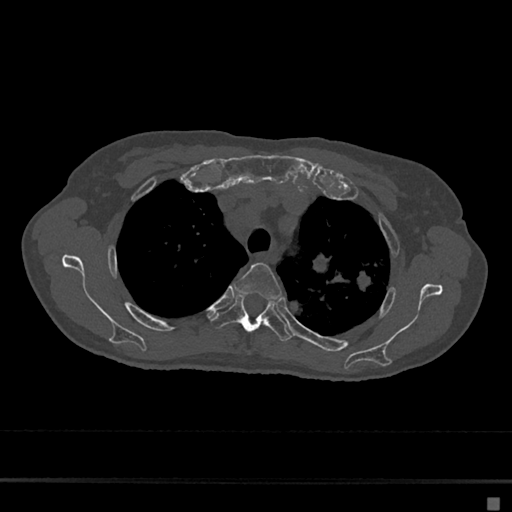
CT including the spine, one axial slice. Slice 517 of 797 in the series (ordered by position). Reconstruction kernel Br40s/3. 120 kVp. Bone window (W 1800 / L 400 HU). 0.5 mm slice thickness. 512 × 512 image matrix, field of view 360 × 360 mm. Patient: female, 68 years. Case-level facts recorded for this patient, not image findings: primary cancer: renal.
Structures marked on this image (semi-automatic segmentation, software-assisted and operator-edited):
- T3 vertebra: bounding box (x1, y1, x2, y2) in pixels: (232, 263, 282, 299)
- T4 vertebra: (210, 296, 291, 342)